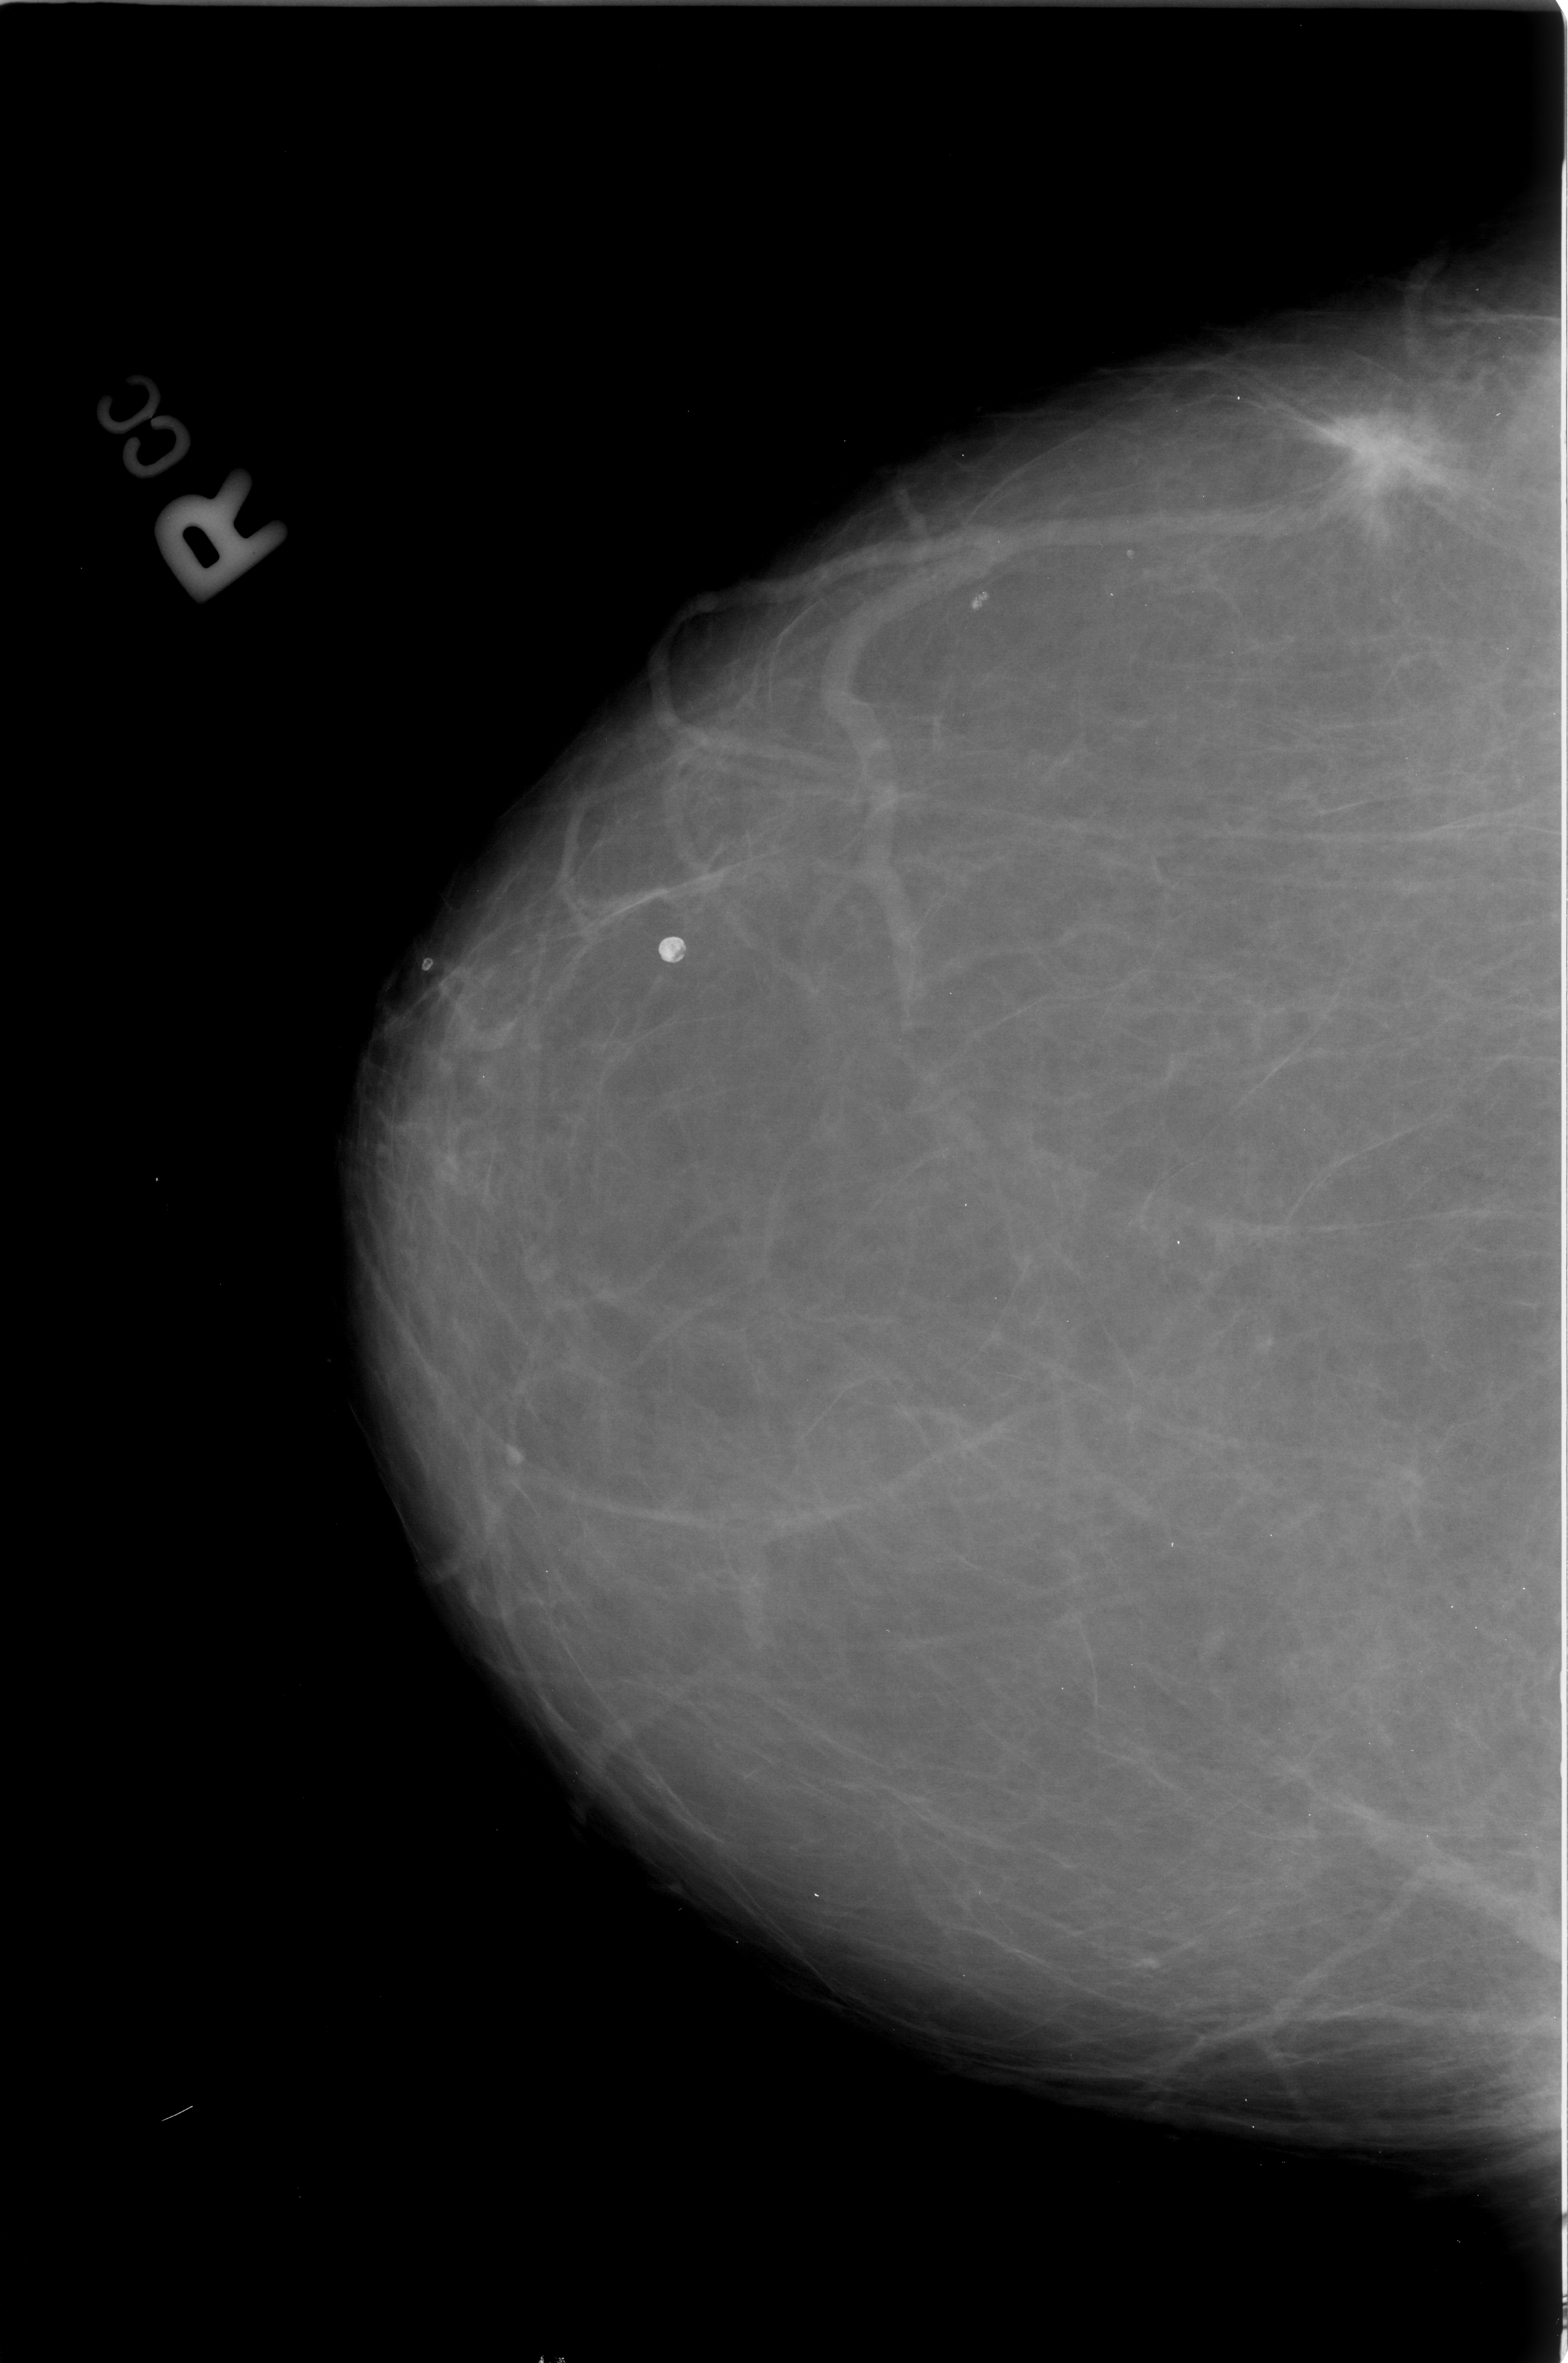
Mammogram (digitized film); right breast; craniocaudal (CC) view; breast composition: almost entirely fatty (BI-RADS density category 1 of 4).
Mass, shape irregular / architectural distortion, margins spiculated; BI-RADS assessment category 5; subtlety rating 5 on a 1 (subtle) to 5 (obvious) scale; pathology (as recorded): malignant.